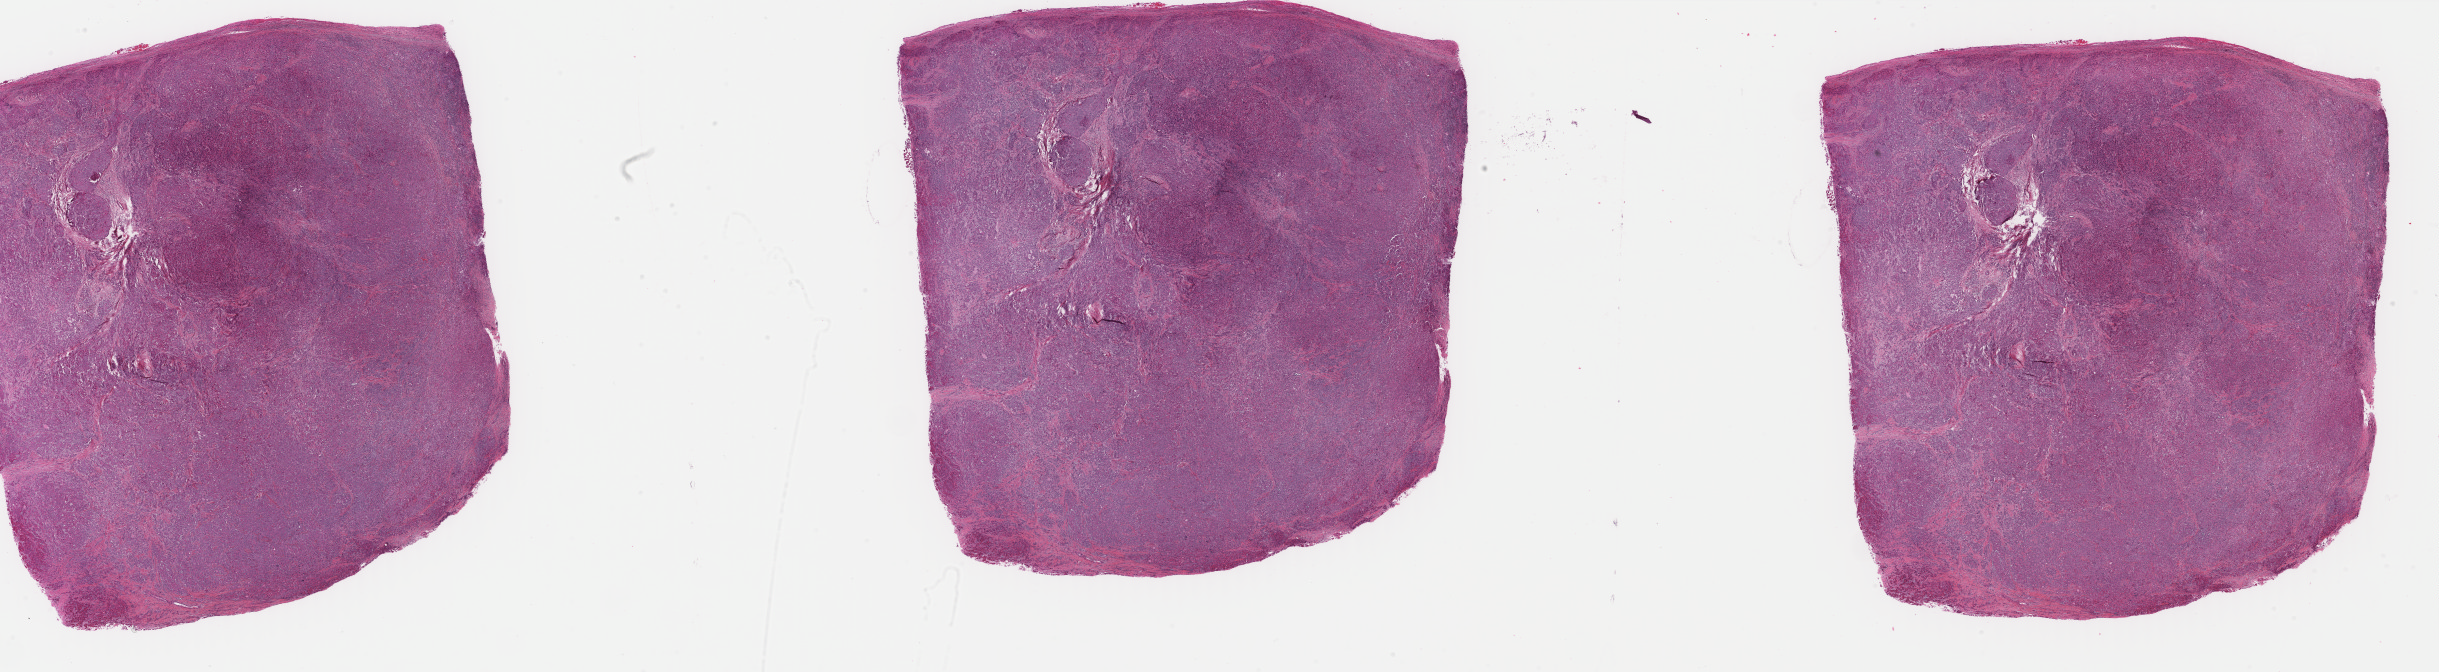
Whole-slide histology image, H&E-stained — low-resolution overview of the scanned area, about 38.7 x 10.7 mm, FFPE section, primary tumour sample from the liver. Female, age 74 years at initial diagnosis. Histologic grade: G3 (poorly differentiated).
Diagnosis: Hepatocellular carcinoma, NOS. AJCC pathologic stage: IIIA (6th edition).